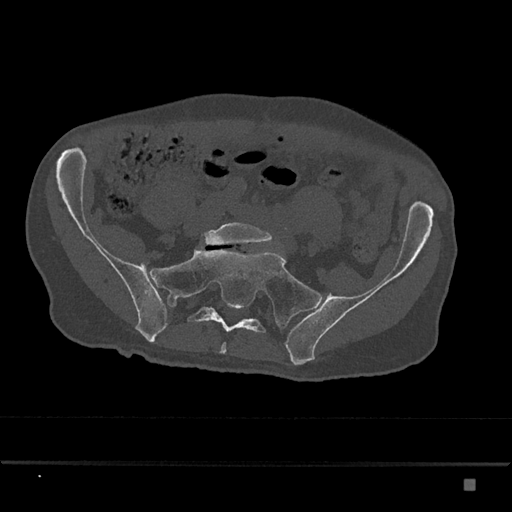
CT including the spine, one axial slice; slice 220 of 797 in the series (ordered by position); reconstruction kernel Br40s/3; bone window (W 1800 / L 400 HU); 0.5 mm slice thickness; 512 × 512 image matrix. Patient: male, 72 years. Case-level facts recorded for this patient, not image findings: primary cancer: prostate.
Annotated regions visible in this slice (semi-automatic segmentation, software-assisted and operator-edited):
- L5 vertebra: bounding box (x1, y1, x2, y2) in pixels: (203, 222, 273, 246)